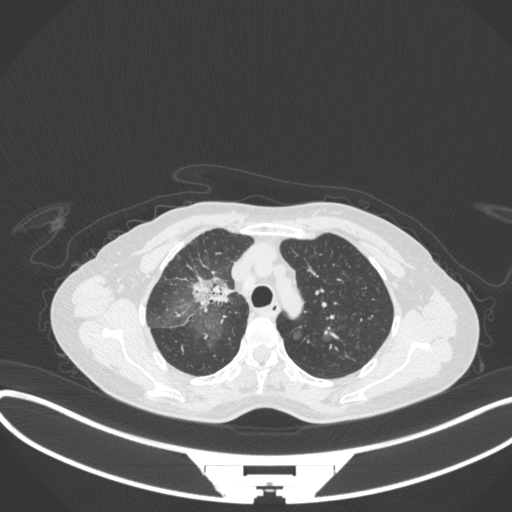
Chest CT, one axial slice; position 241 of 311 along the scan axis; reconstruction kernel B31f; lung window (W 1500 / L -600 HU); 512 × 512 image matrix, field of view 400 × 400 mm. Patient: female, 59 years. From the clinical record (not read from this slice): clinical TNM (as recorded): T3 N0 M0; histopathological grade: G1.
Annotated regions visible in this slice (rectangle marked by the reading radiologist):
- lung tumour (recorded histology: adenocarcinoma): box from (x=186, y=266) to (x=234, y=316) px